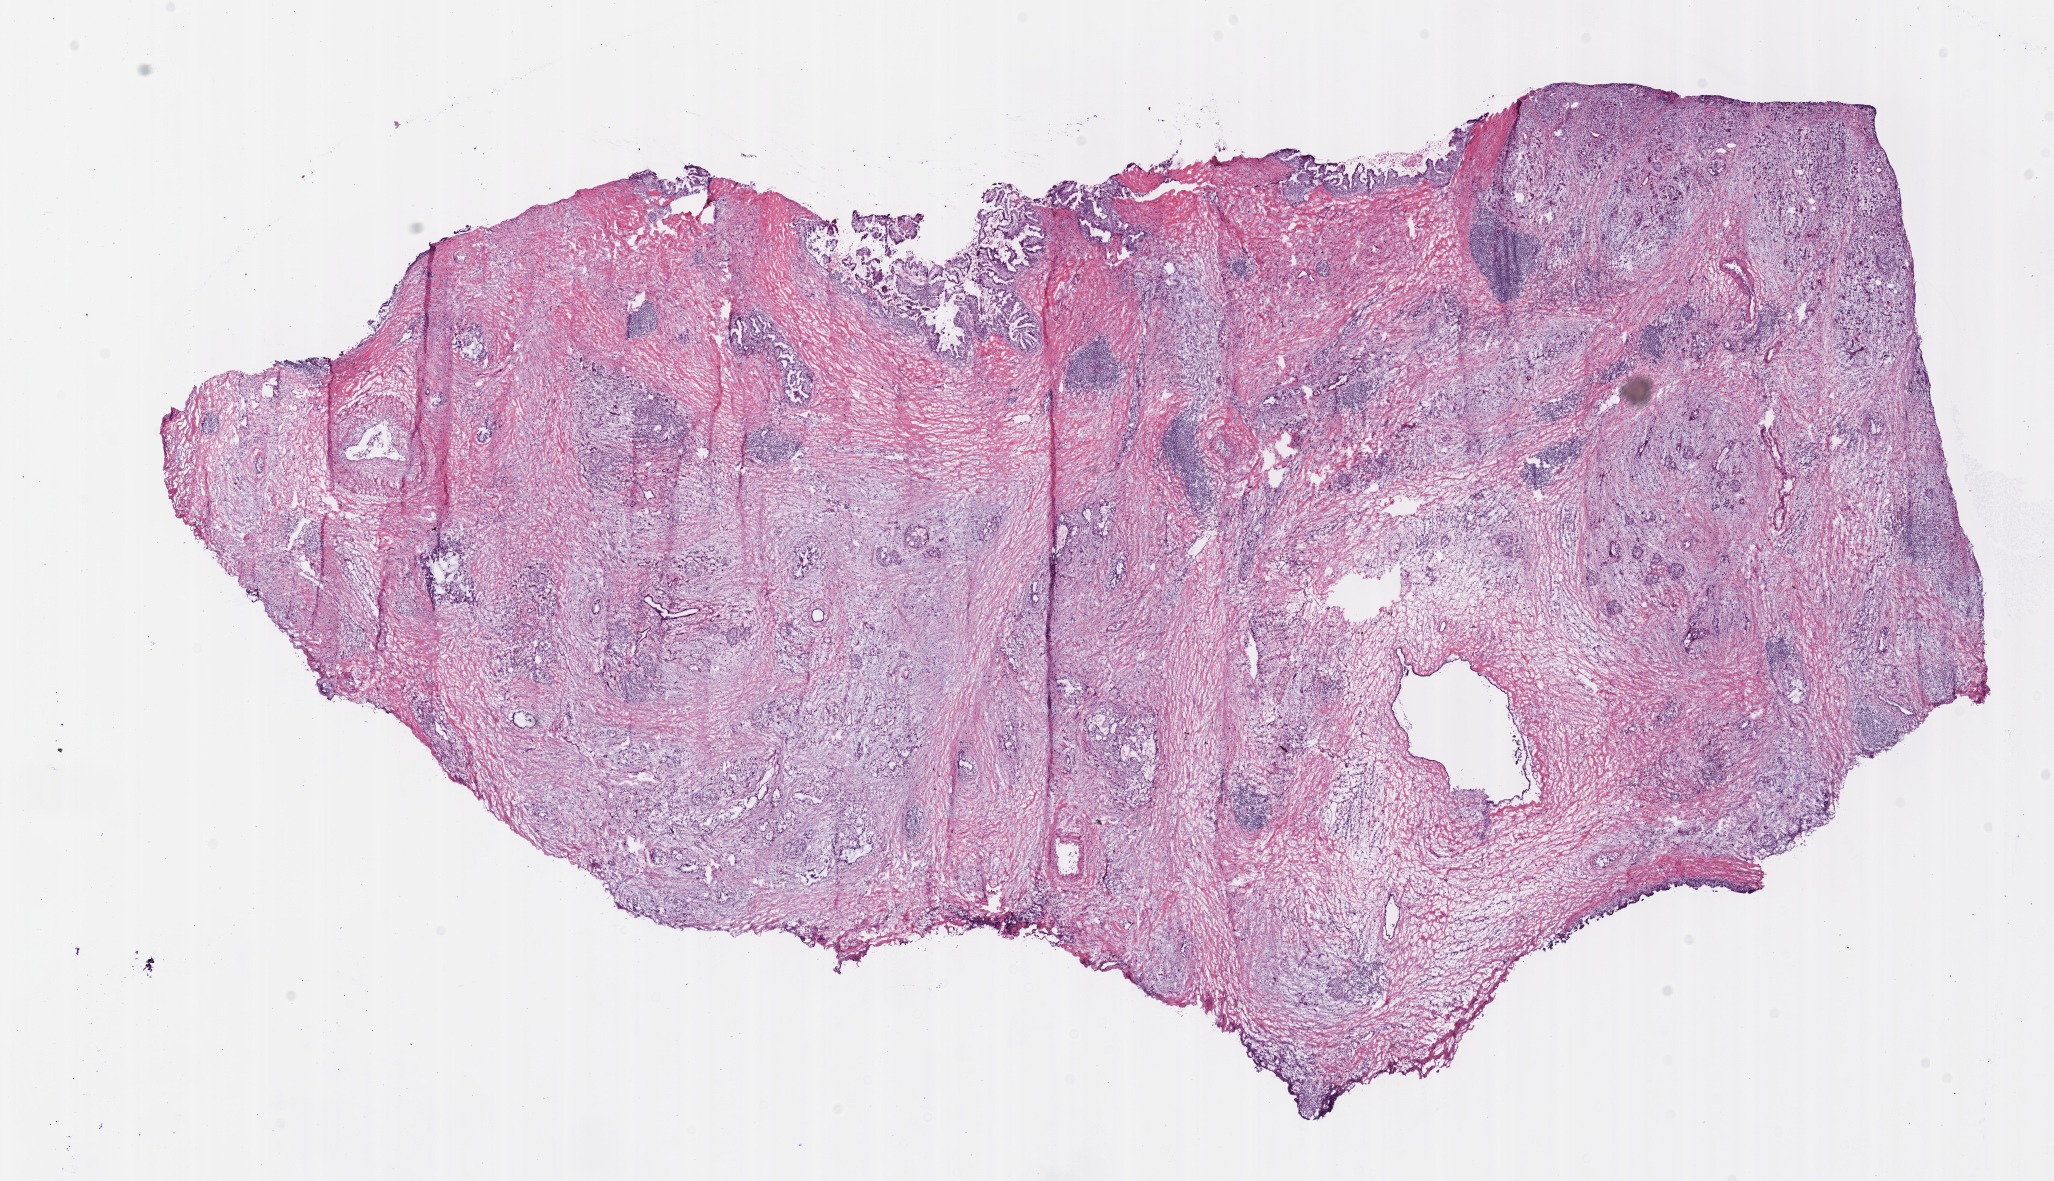
H&E whole-slide image, shown as a low-resolution overview of the whole scanned area (about 16.2 x 9.3 mm, from a 40x scan), frozen section from the bottom of the tissue portion, sample: primary tumour, pancreas. Male patient; age at initial diagnosis 41 years. Histologic grade: G2 (moderately differentiated). Pathologist review of this section (percent, as recorded): tumour cells 85%, tumour nuclei 50%, normal cells 0%, stromal cells 15%, necrosis 0%. Infiltration values recorded for this section: lymphocyte infiltration 15%, monocyte infiltration 0%, neutrophil infiltration 0%.
AJCC pathologic stage: IIB (6th edition). Diagnosis: Infiltrating duct carcinoma, NOS (head of pancreas). Lymph nodes positive (case pathology): 14 of 20 examined.